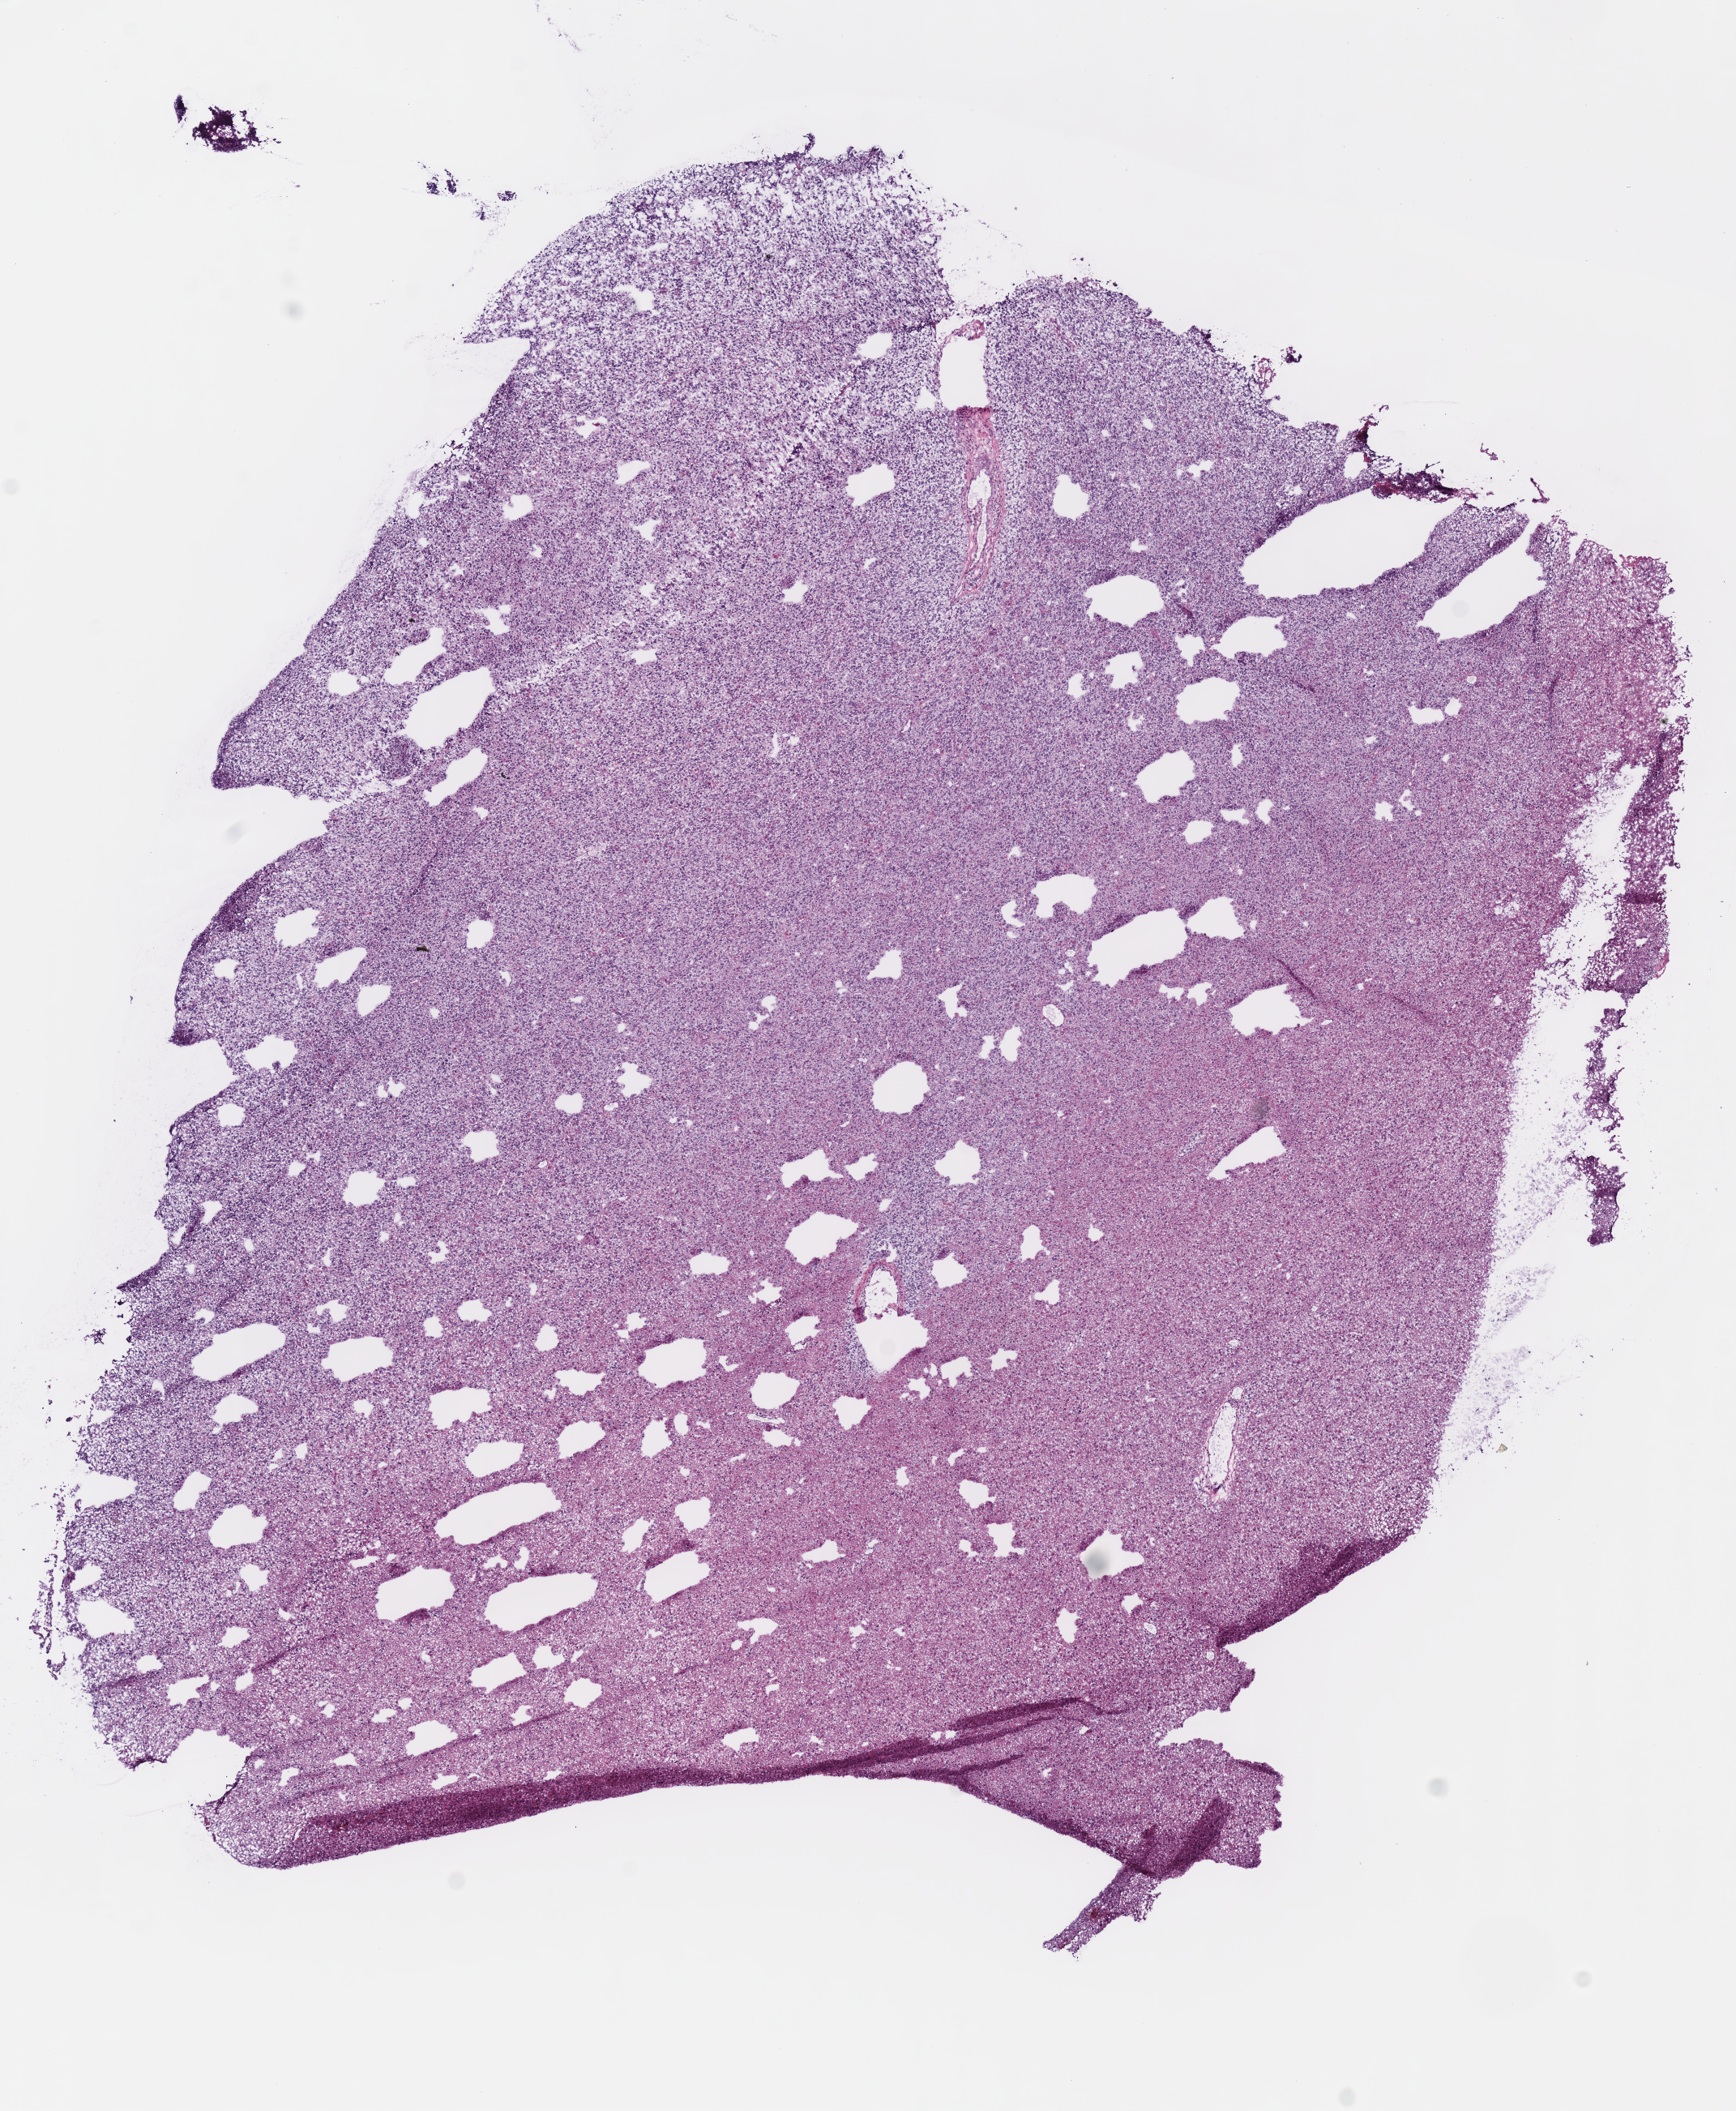
Digitized H&E tissue section (whole slide), shown as a low-resolution overview of the whole scanned area (about 8.4 x 10.3 mm), frozen section from the top of the tissue portion, brain, primary tumour sample. Female, age 30 years at initial diagnosis. Histologic grade: G2 (moderately differentiated). Slide review estimates, as recorded: tumour cells 100%, tumour nuclei 80%, normal cells 0%, stromal cells 0%, necrosis 0%.
Histologic diagnosis: Astrocytoma, NOS.